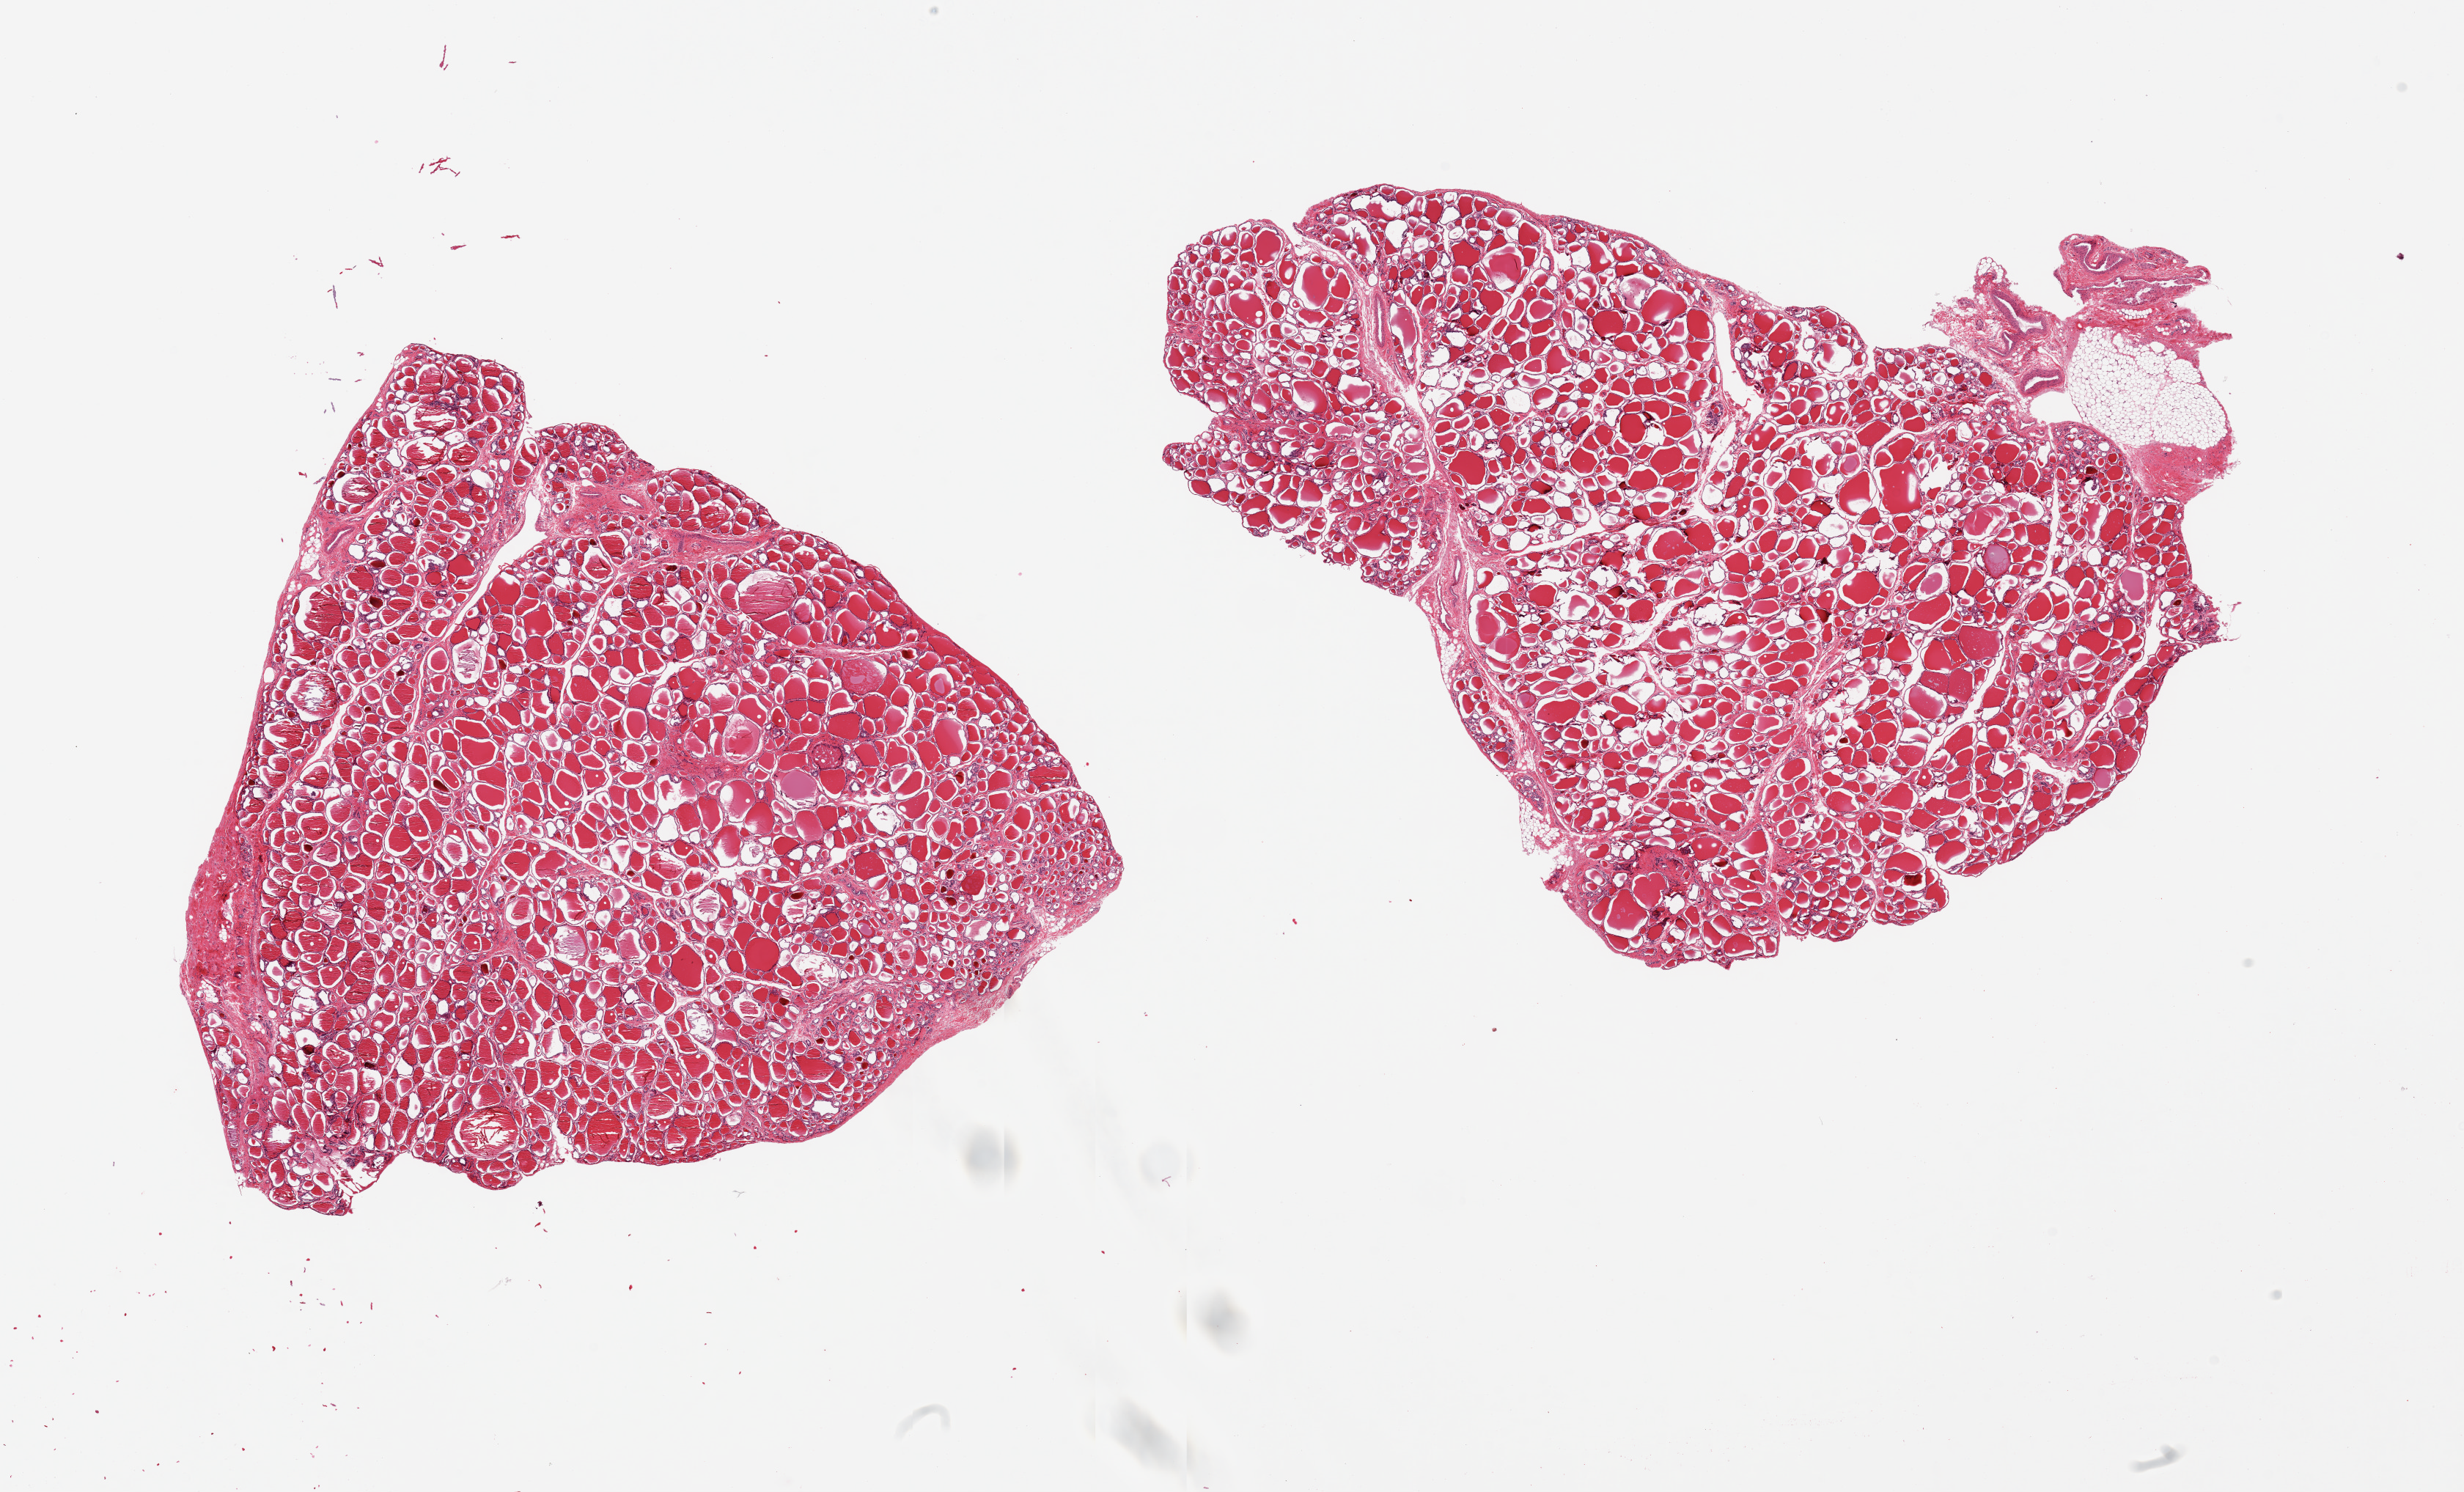
H&E whole-slide image, brightfield, low-resolution overview of the scanned area, about 26.6 x 16.1 mm (from a 20x scan); PAXgene-fixed, paraffin-embedded tissue; sampled site (target tissue): thyroid; tissue donor sample. Male donor.
Pathologist's review note for this sample: 2 pieces, 2 mm nubbin of fat/vessel on one aliquot.